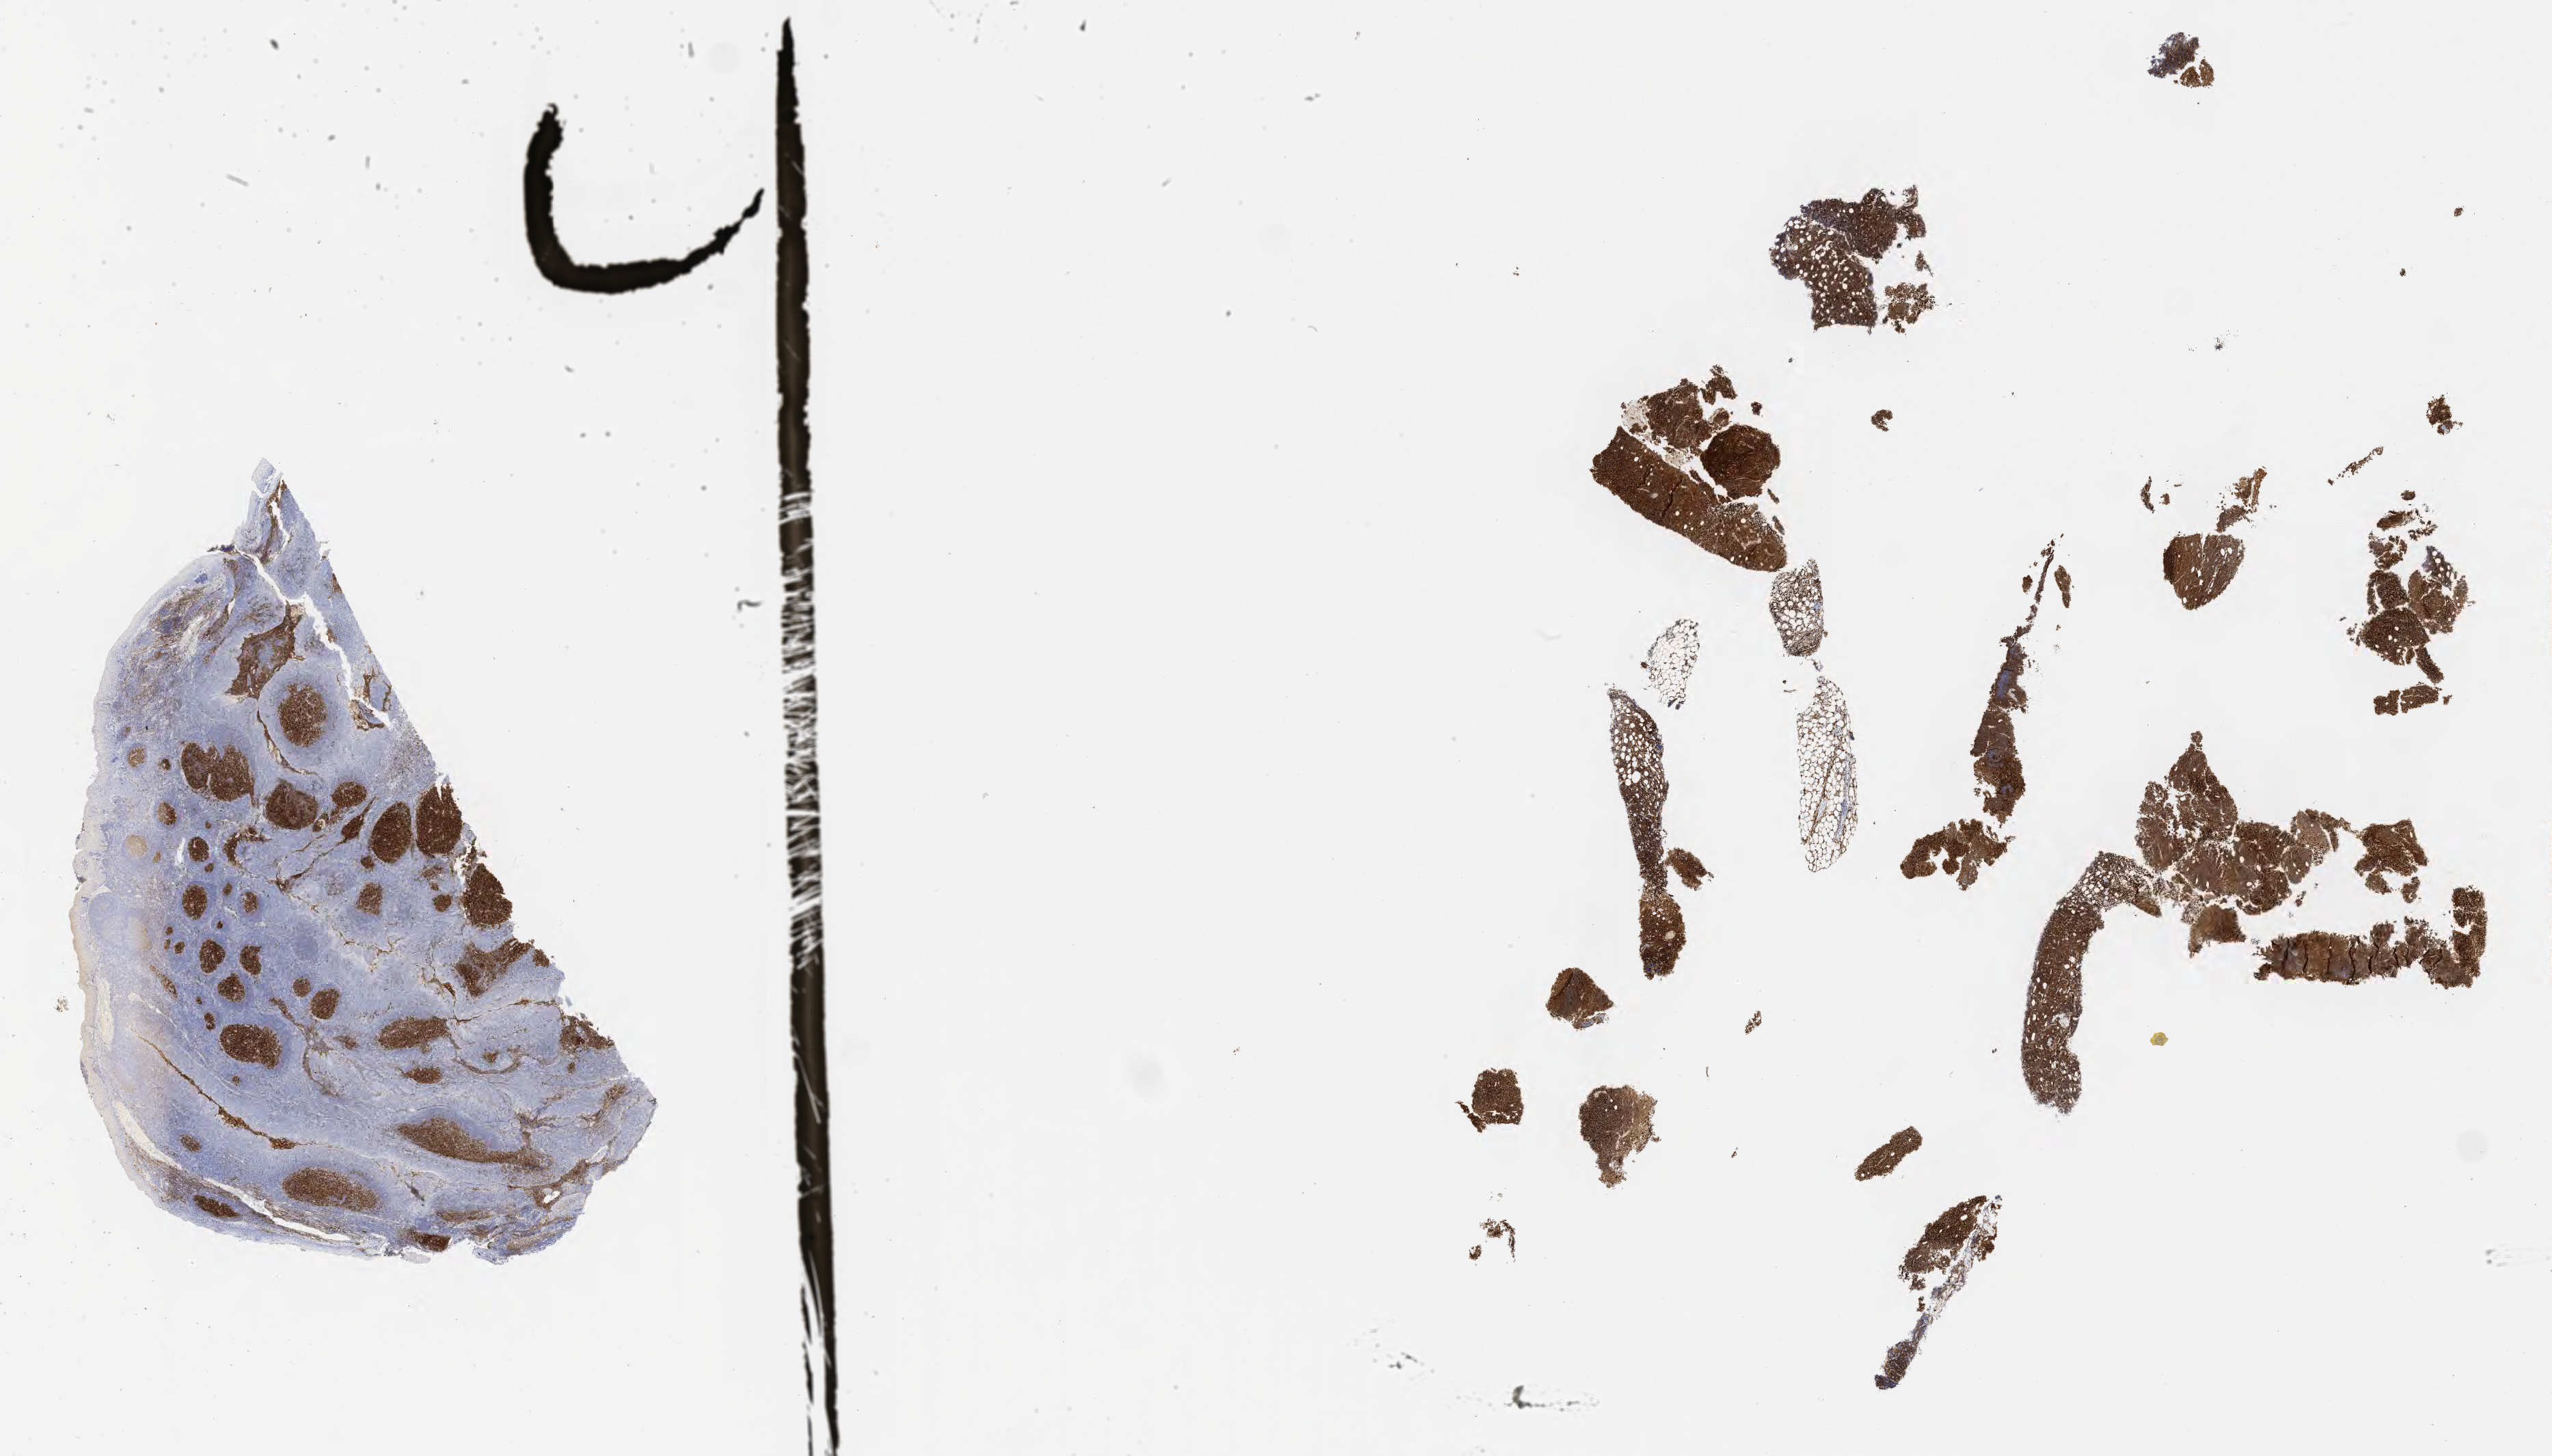
IHC for CD10, whole-slide image, whole scanned area (about 30.2 x 17.2 mm) shown as a low-resolution overview; tumor tissue; anatomic site: pelvis. Patient: female, age 64 years.
- histologic diagnosis: Burkitt lymphoma, NOS